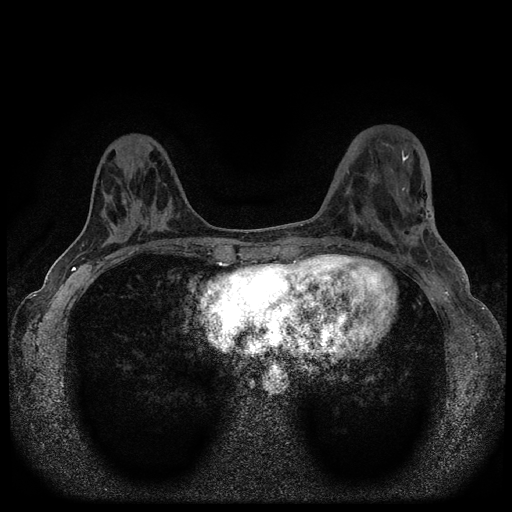
Breast MRI (dynamic contrast-enhanced, multi-phase), one axial slice. Dynamic contrast-enhanced series, time point 2 of 5 at this slice position (early post-contrast). 1.5 T. TE 2.7 ms, TR 5.6 ms. 512 × 512 image matrix. Patient: female, 40 years.
Structures marked on this image (semi-automatic segmentation, software-assisted and operator-edited):
- breast lesion (labelled benign in the annotation): bounding box <134,198,142,210> (left, top, right, bottom; pixels)